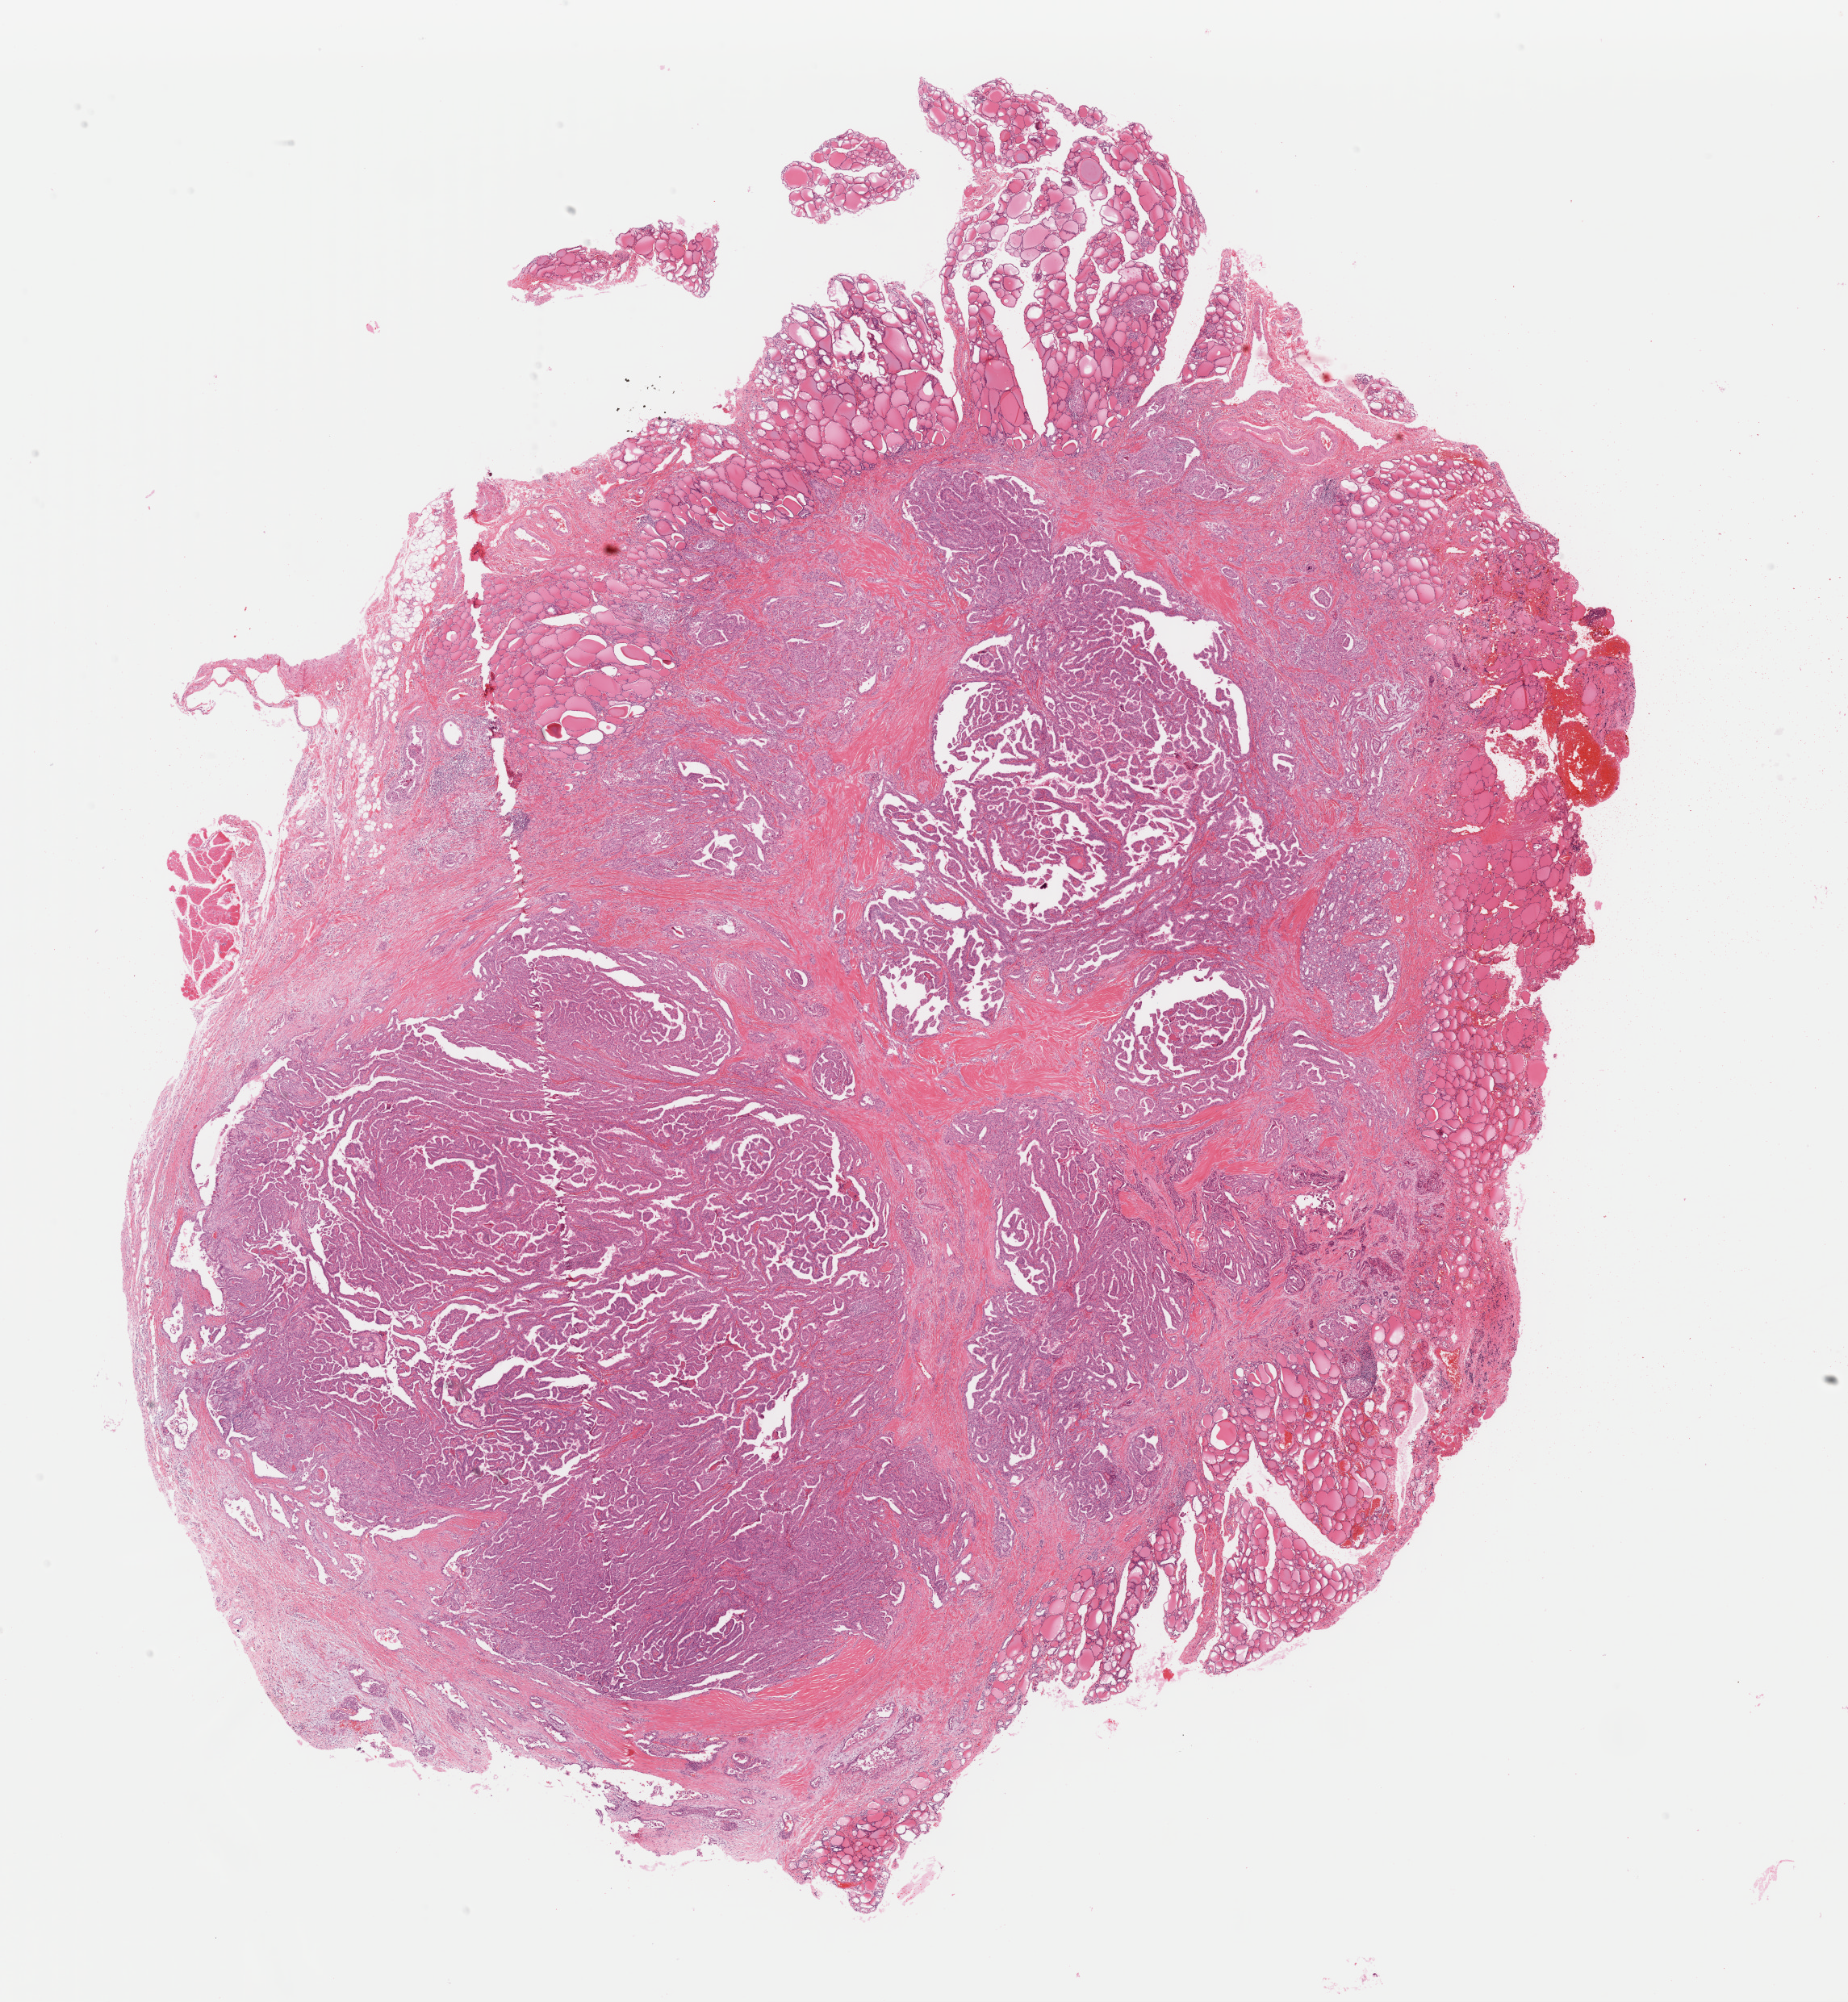
Digitized H&E tissue section (whole slide) — low-resolution overview of the scanned area, about 18.1 x 19.6 mm. FFPE section. Thyroid, primary tumour sample. Patient: female, age at initial diagnosis 53 years.
• pathologic diagnosis: Papillary adenocarcinoma, NOS (thyroid gland)
• AJCC pathologic stage: IVA (7th edition)
• TNM: T2 N1b M0
• laterality: bilateral
• lymph nodes positive (case pathology): 1 of 10 examined